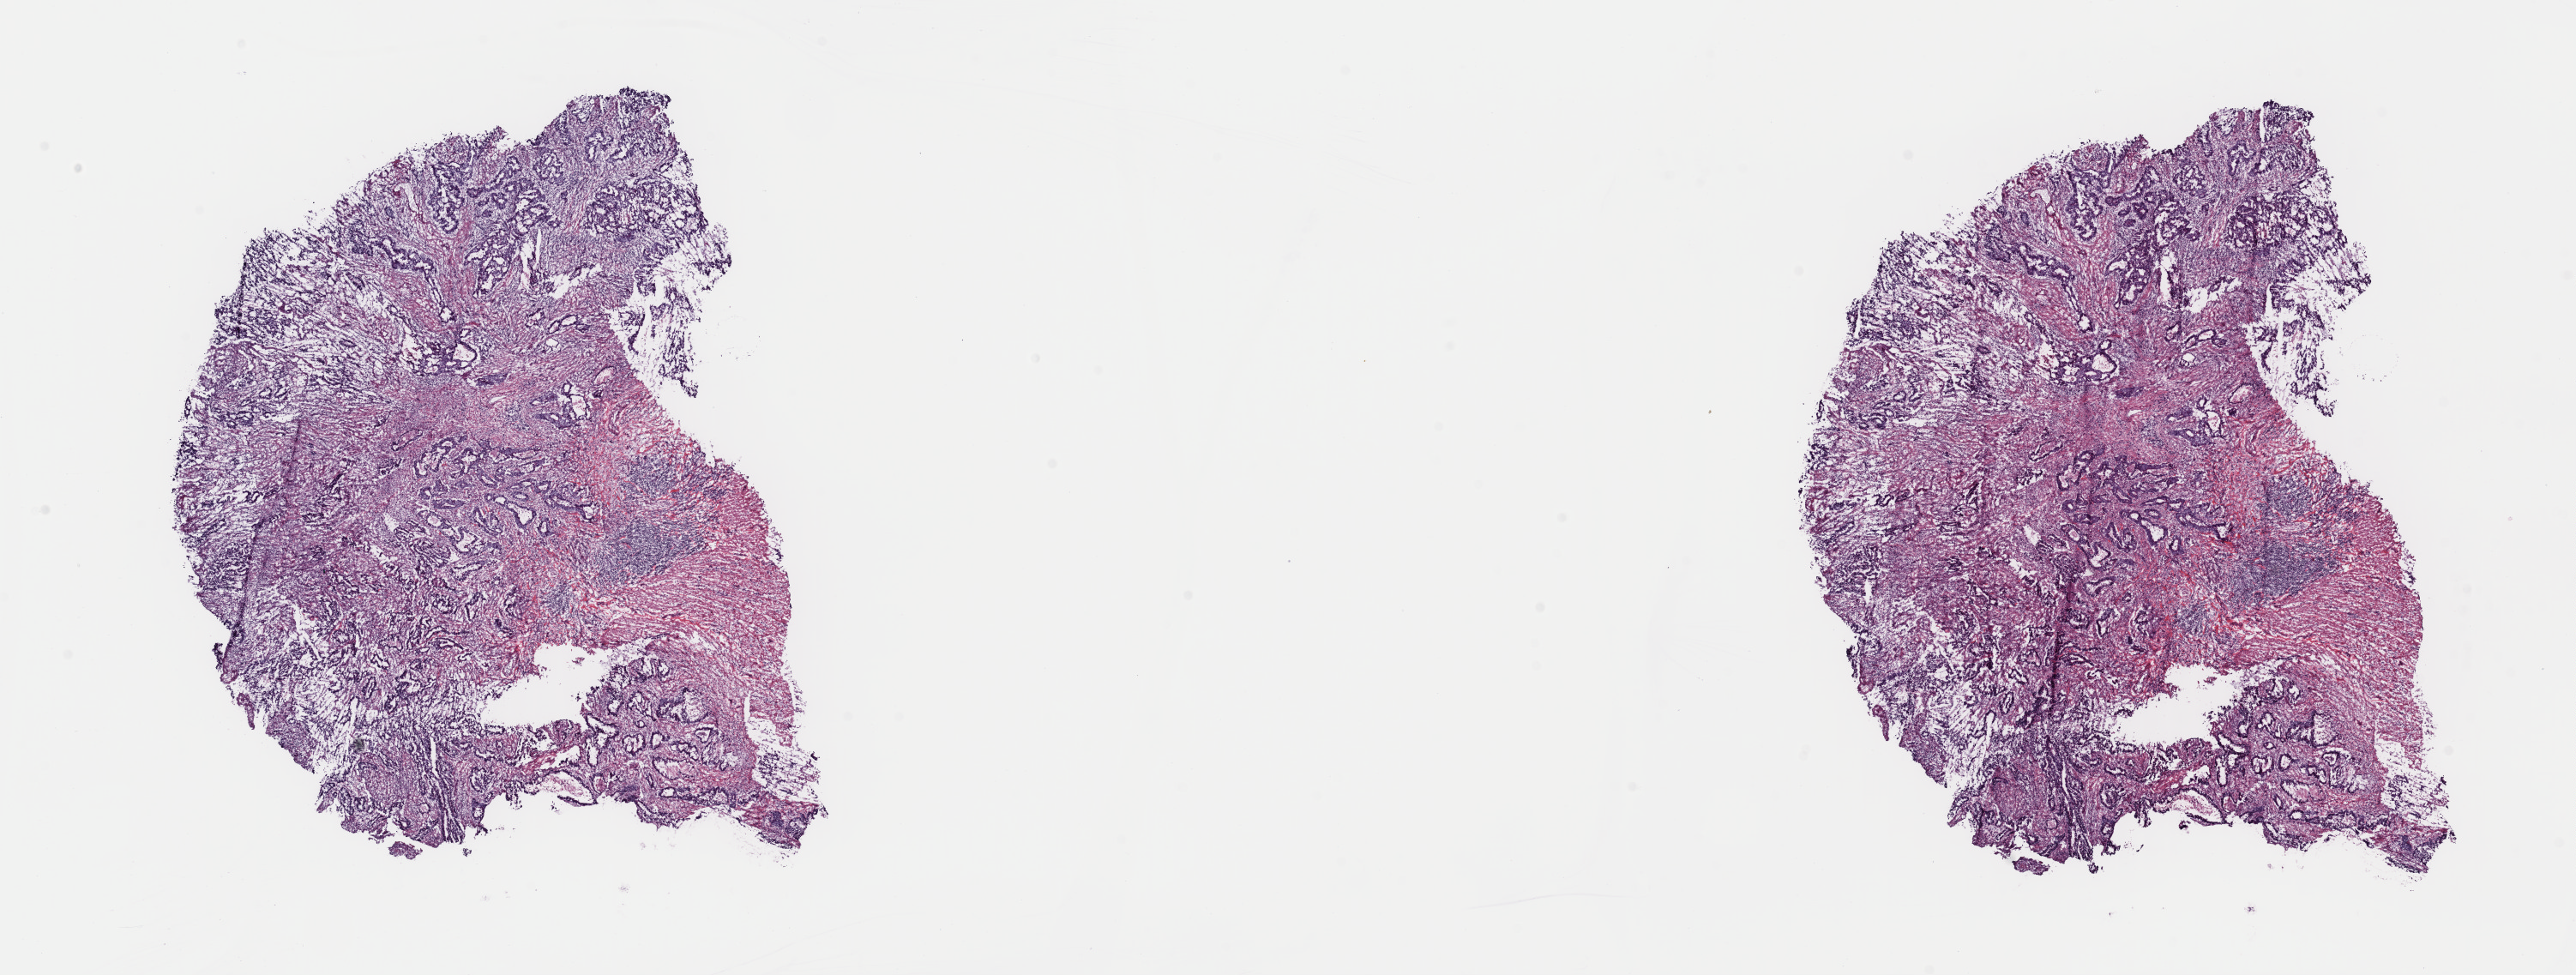
H&E whole-slide image — a low-resolution overview of the entire scanned area, about 23.7 x 9.0 mm (from a 40x scan). Frozen section from the top of the tissue portion. Rectum, primary tumour sample. Patient: male, age at initial diagnosis 56 years. Composition of this section per pathologist review: tumour cells 97%, tumour nuclei 60%, normal cells 0%, stromal cells 0%, necrosis 3%. Inflammatory infiltration, as recorded: lymphocyte infiltration 10%, monocyte infiltration 1%, neutrophil infiltration 2%.
AJCC pathologic stage: IIA (6th edition). Histologic diagnosis: Adenocarcinoma, NOS (rectosigmoid junction). TNM: T3 N0 M0.